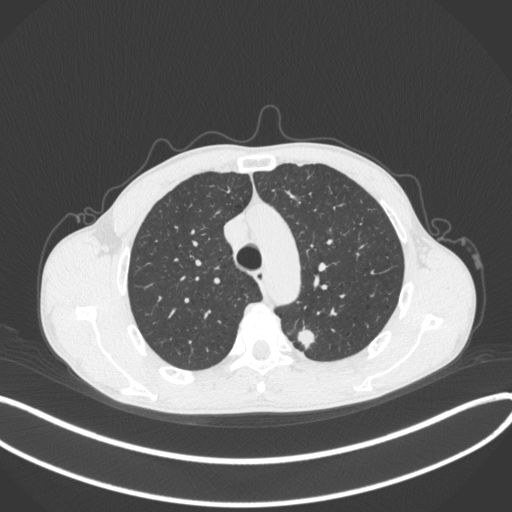
Chest CT, one axial slice. Slice 298 of 429 in the series (ordered by position). Reconstruction kernel B31f. 120 kVp. Lung window (W 1500 / L -600 HU). 1 mm slice thickness. 512 × 512 image matrix, field of view 400 × 400 mm. Patient: male, 51 years. From the clinical record (not read from this slice): clinical TNM (as recorded): T2a N1 M1.
Structures marked on this image (bounding box drawn by a radiologist):
- lung tumour (recorded histology: adenocarcinoma): bounding box (x1, y1, x2, y2) in pixels: (296, 323, 319, 352)